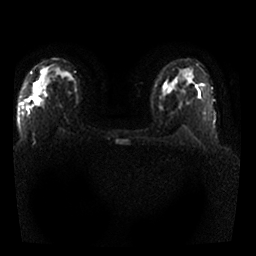
Breast MRI, one axial slice; slice 18 of 25 in the series (ordered by position); diffusion-weighted series; image 2 of 4 stored at this slice position (different b-values; order by instance number); 1.5 T; 4 mm slice thickness; 256 × 256 image matrix, field of view 330 × 330 mm. Female patient.
Annotated regions visible in this slice (manually delineated by an expert):
- tumour on diffusion-weighted imaging: bounding box [x1, y1, x2, y2] px = [34, 83, 40, 104]